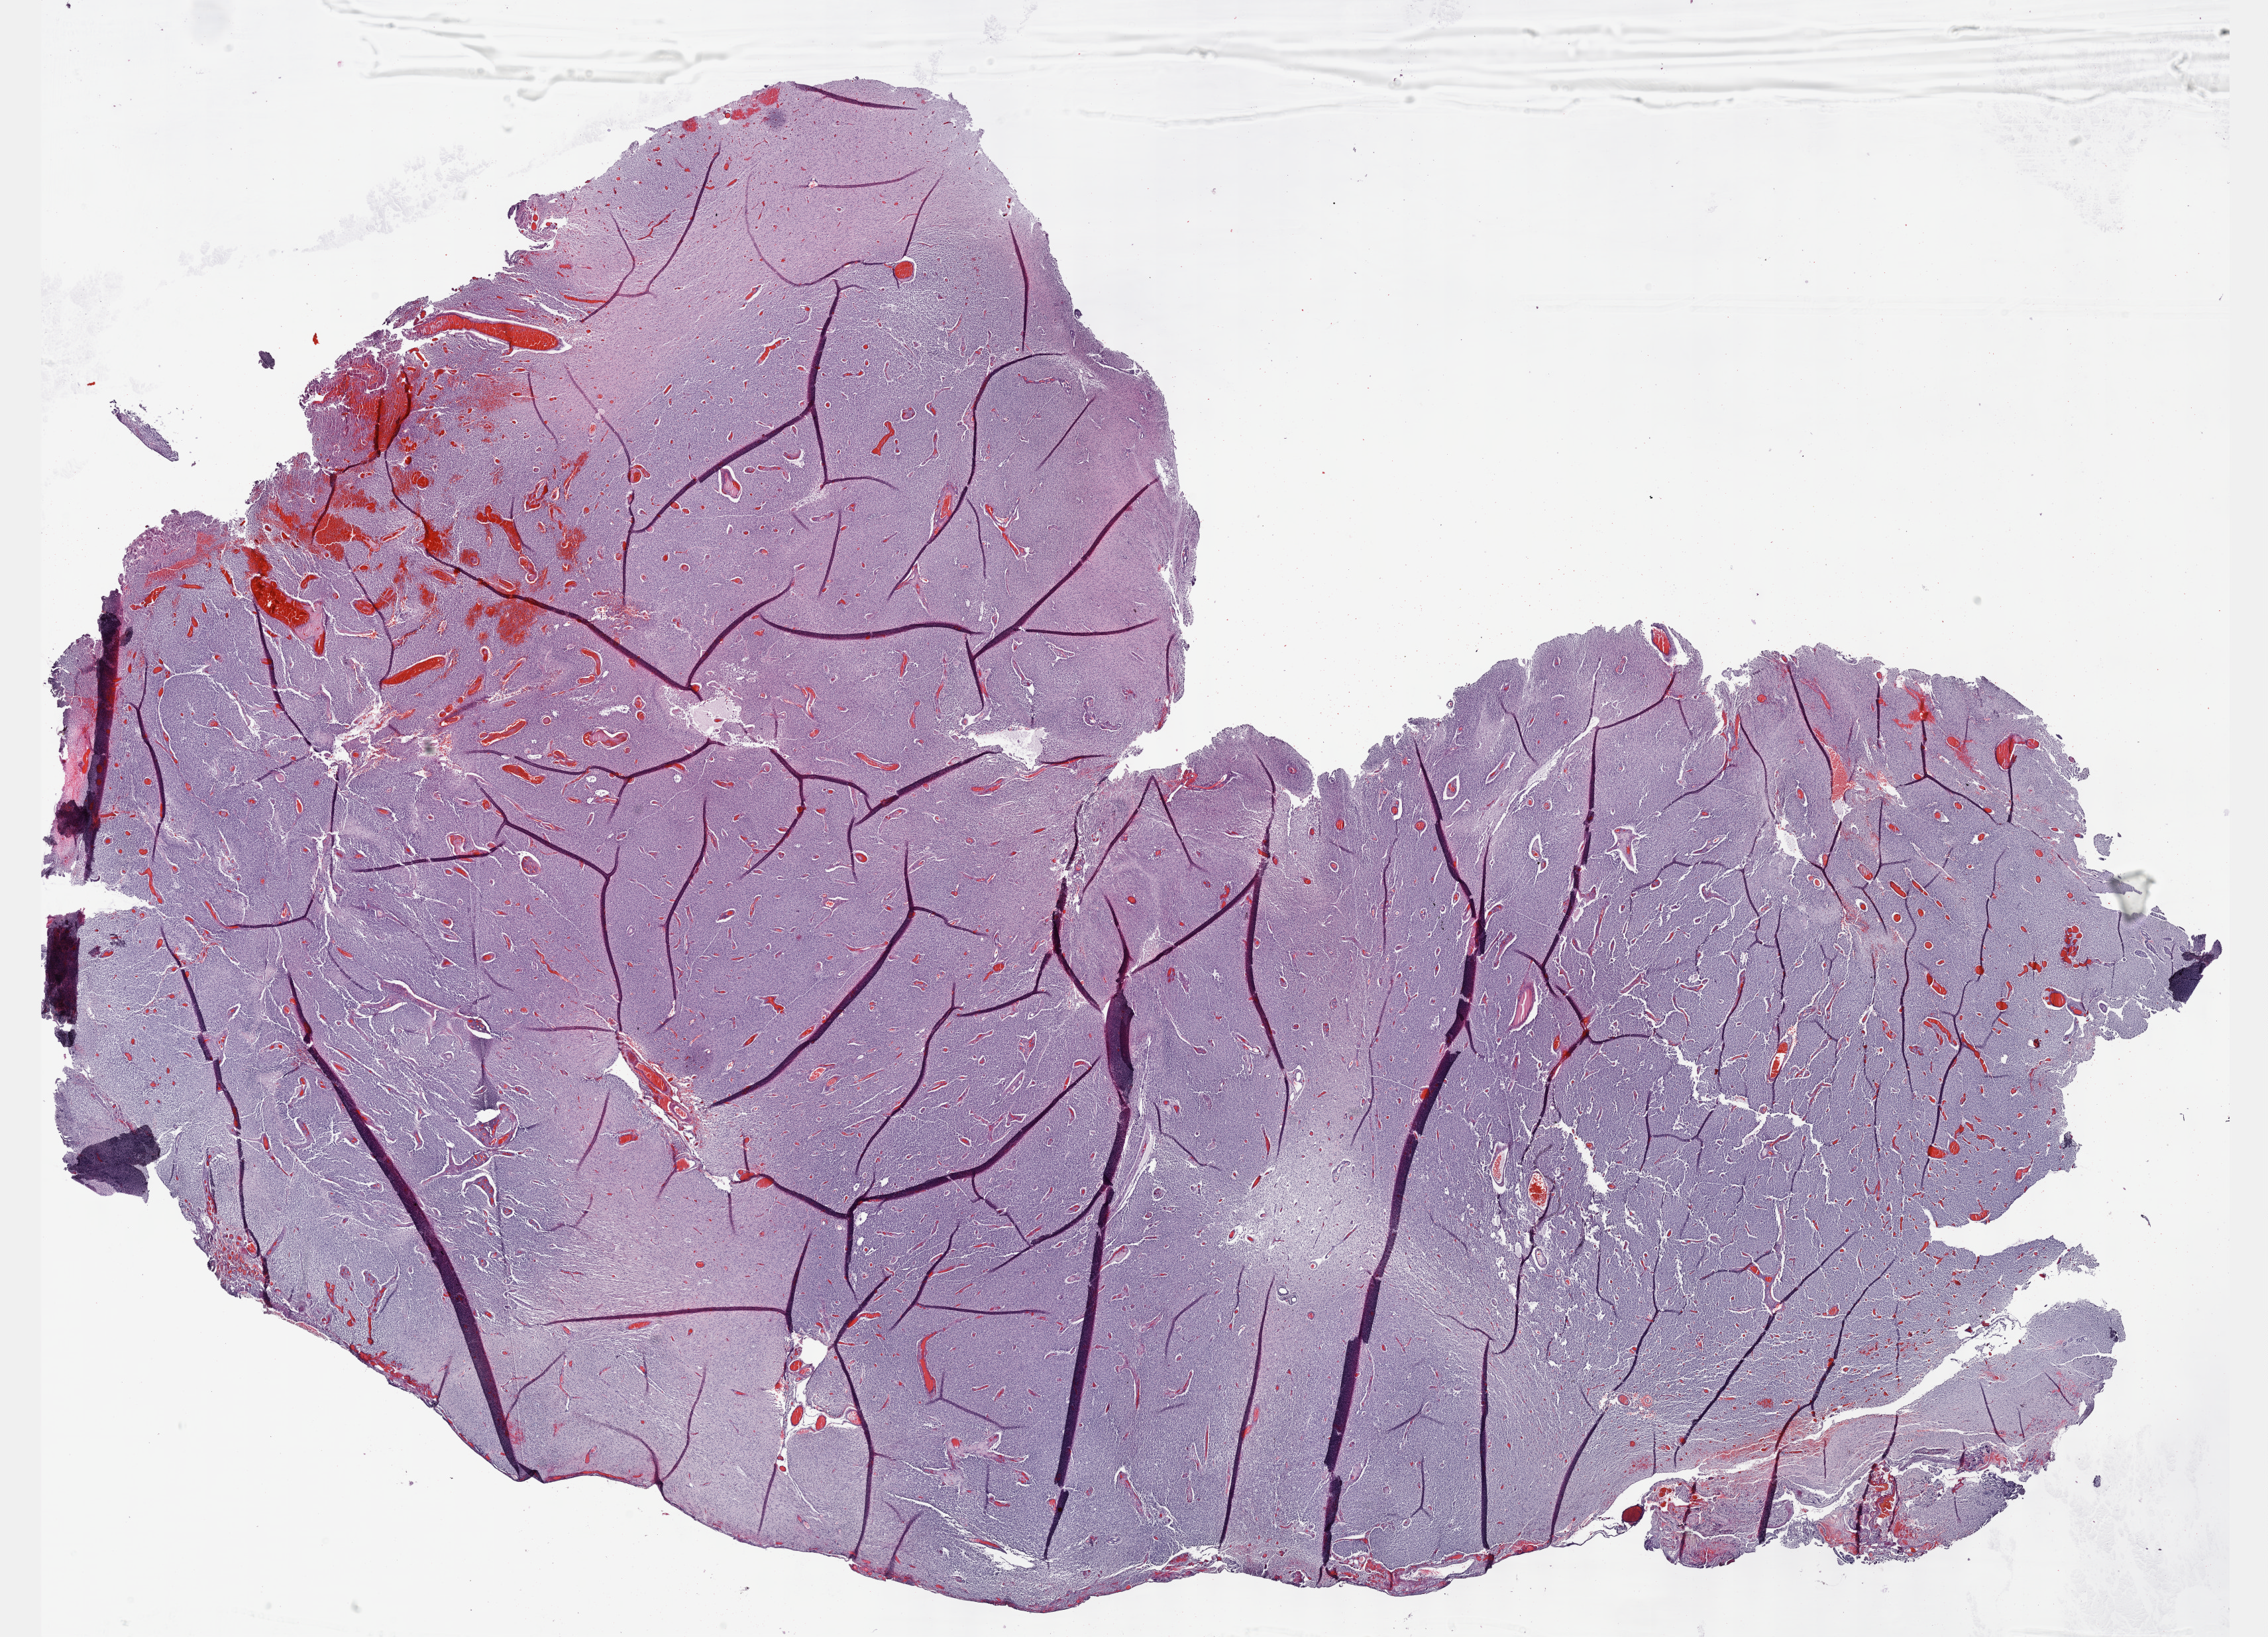
H&E-stained whole-slide image — shown as a low-resolution overview of the whole scanned area (about 27.7 x 20.0 mm, acquisition: 40x scan); formalin-fixed paraffin-embedded (FFPE) diagnostic section; sample: primary tumour, brain. Patient: male, age at initial diagnosis 44 years.
Pathologic diagnosis: Mixed glioma (cerebrum).